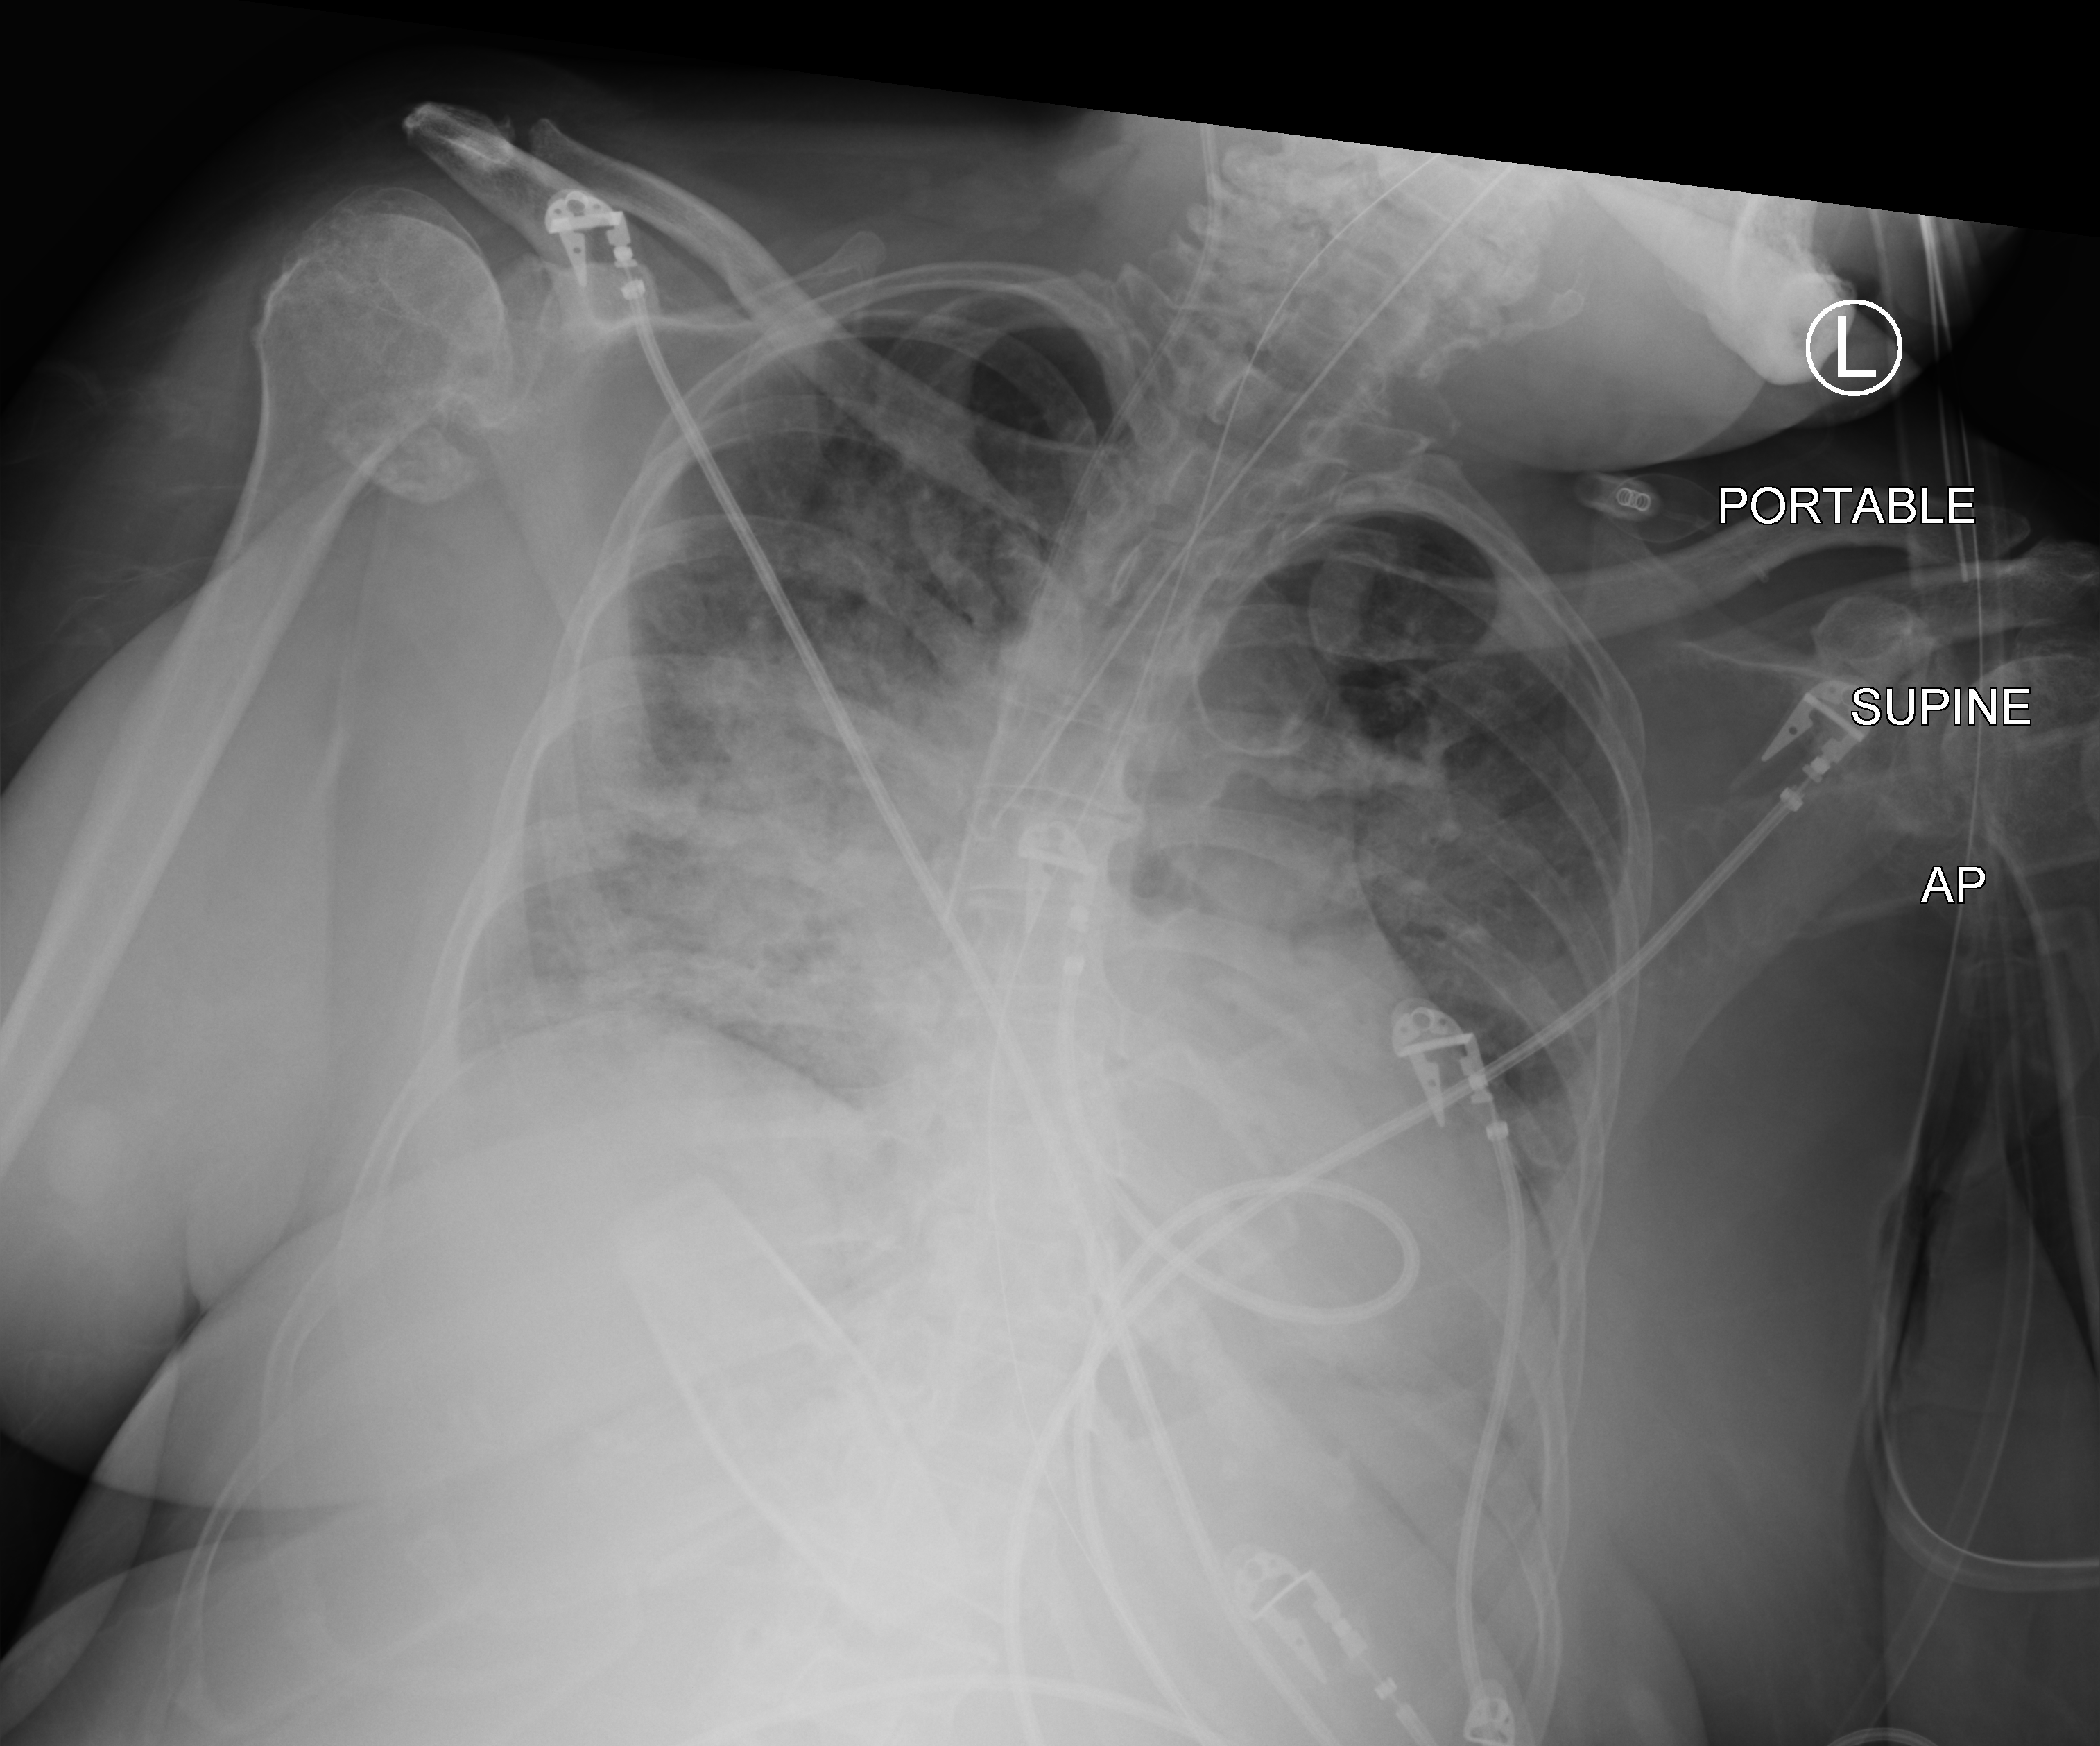
Chest X-ray (portable); anteroposterior (AP) projection. Patient hospitalised with COVID-19; female, aged 60–74 years.
Hospital-stay facts (about this admission, not read from this image; timing relative to this image not recorded): hypertension (admission record): yes; admitted to intensive care during this hospital stay: yes; mechanically ventilated during this hospital stay: yes.